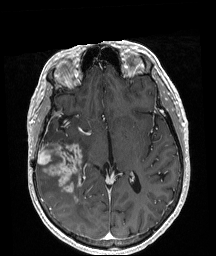
Brain MRI from a brain-tumour surgery series, one axial slice. Slice 107 of 208 in the series (ordered by position). T1-weighted post-contrast. 216 × 256 image matrix. Case-level facts recorded for this patient, not image findings: histopathology: Astrocytoma; WHO grade: 4.
Outlined on this slice (manually delineated by an expert):
- tumour: bounding box [x1, y1, x2, y2] px = [38, 143, 82, 193]